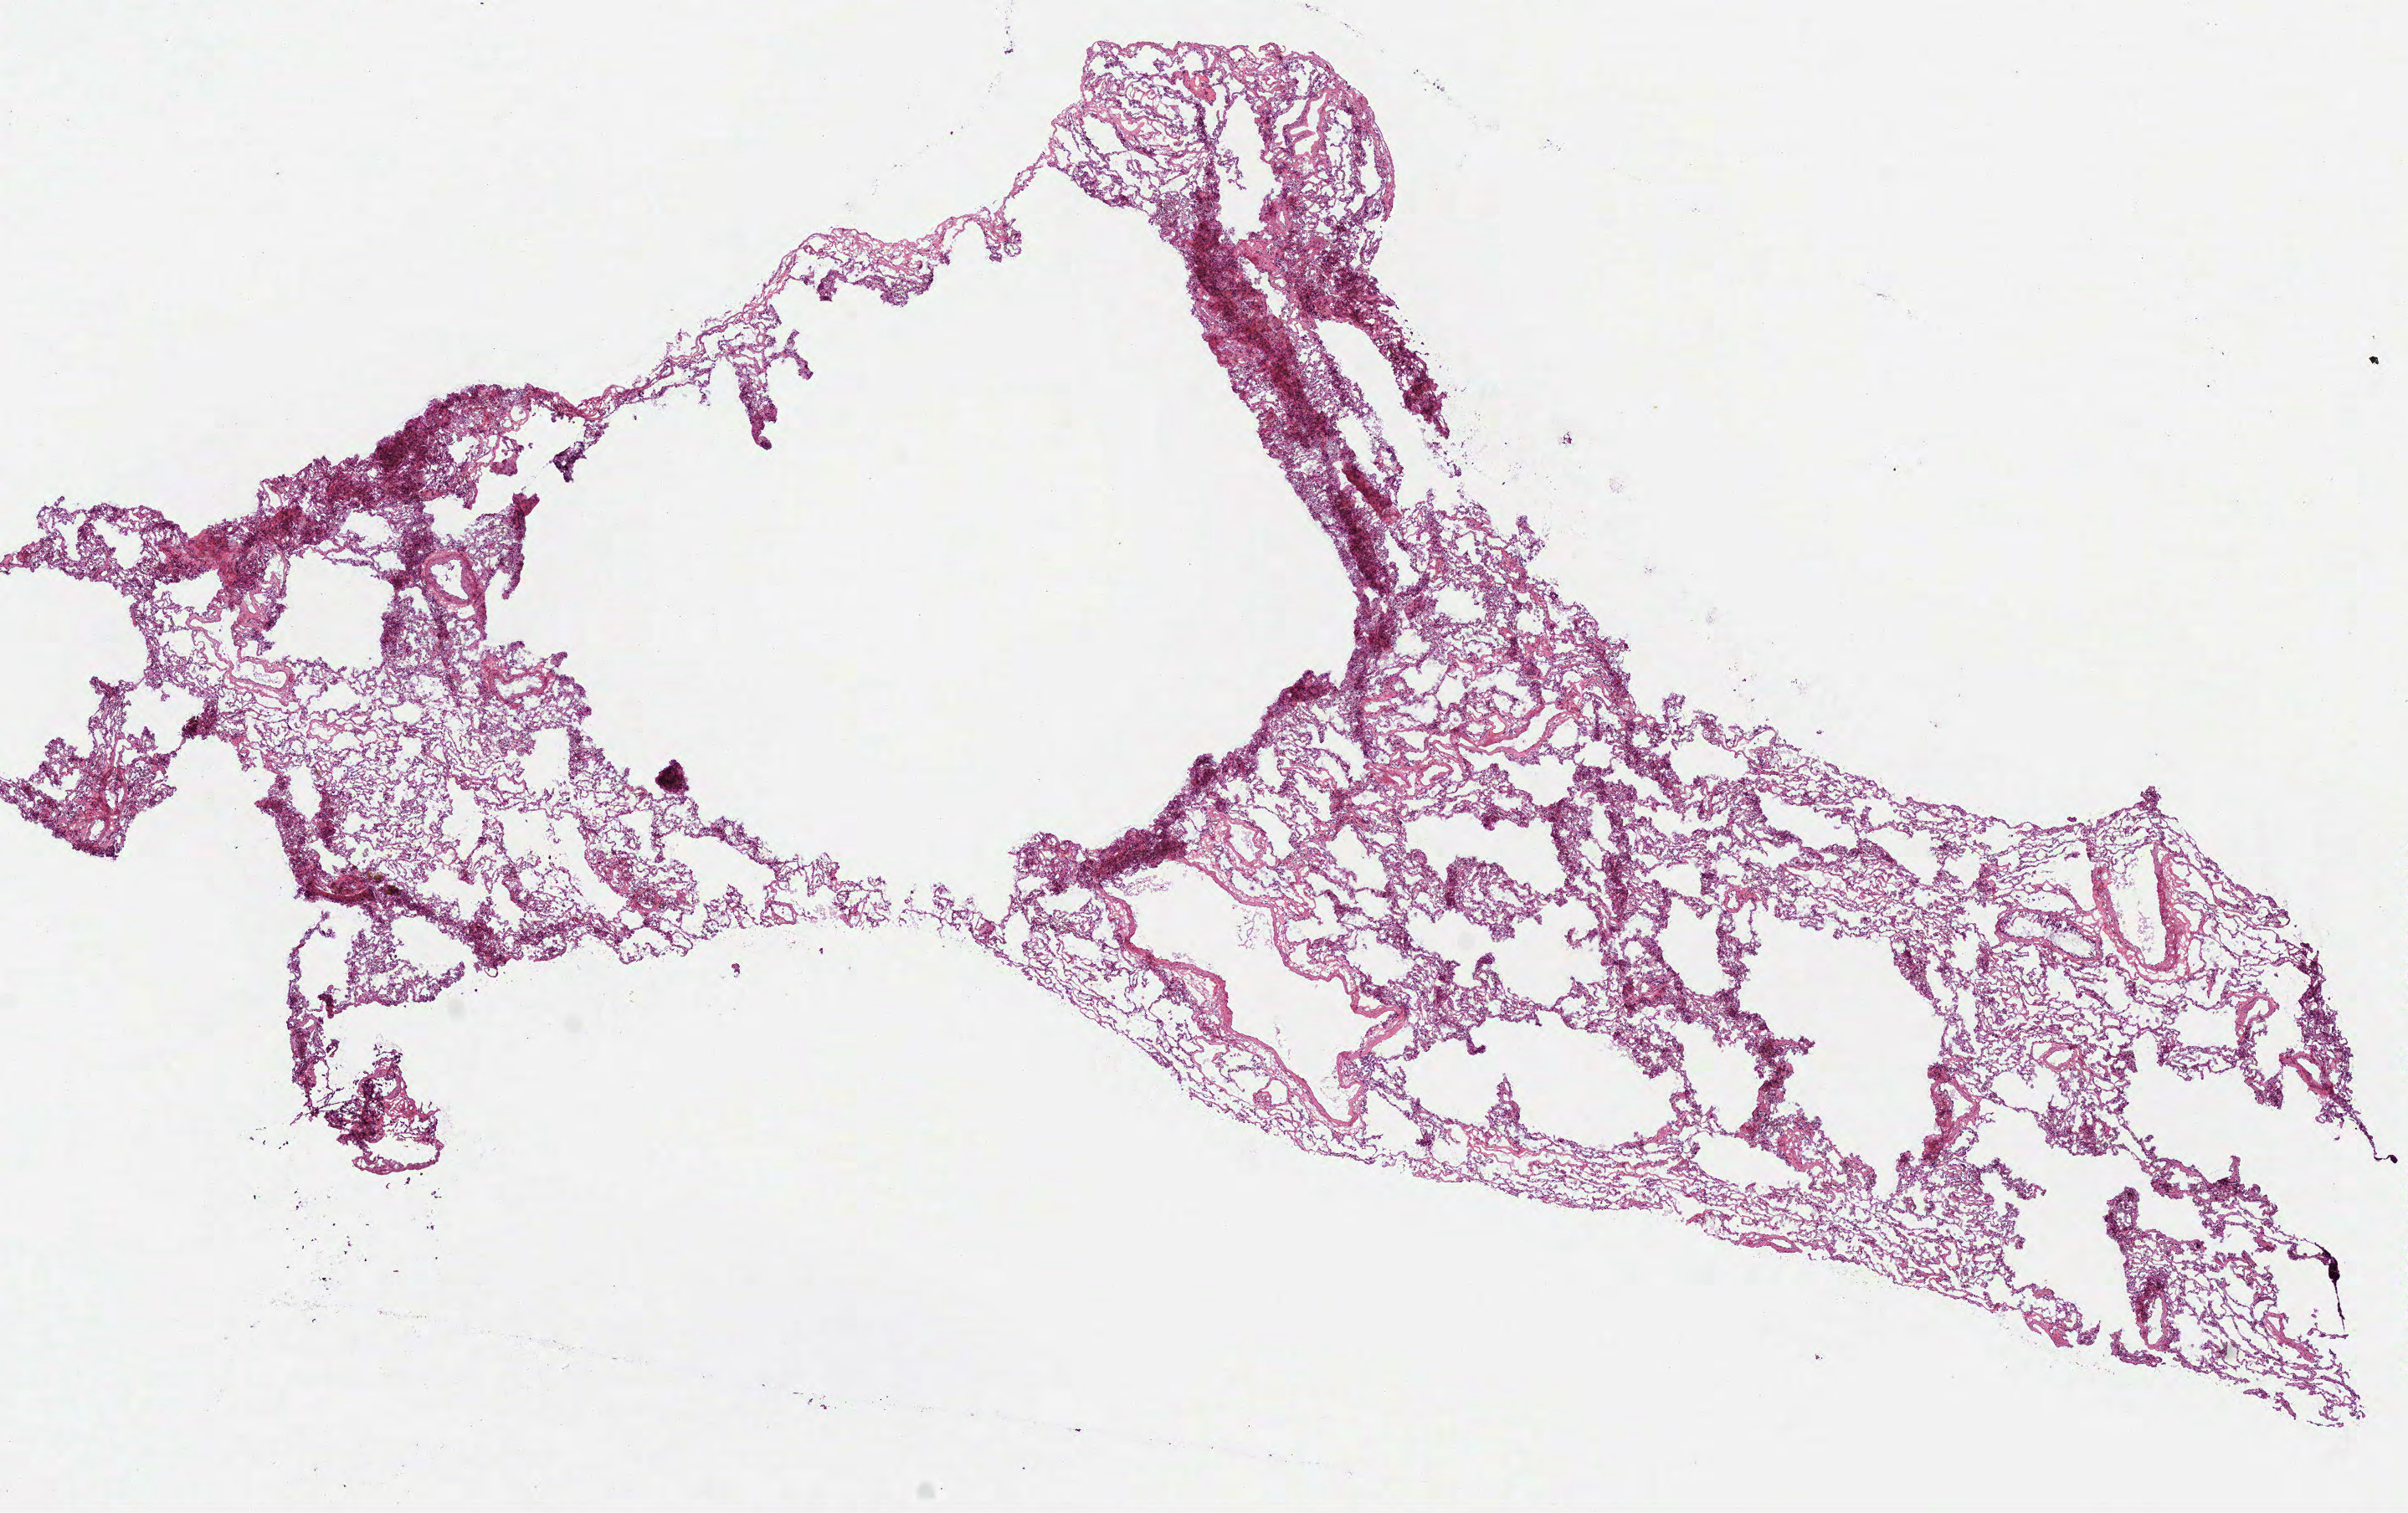
Hematoxylin and eosin (H&E) stained whole-slide image, shown as a low-resolution overview of the whole scanned area (about 11.6 x 7.3 mm); frozen section; solid tissue normal (non-tumour tissue) sample from the lung. Patient: female, age at initial diagnosis 68 years.
• this section: solid tissue normal (non-tumour) sample from the same patient
• patient diagnosis: Adenocarcinoma, NOS (upper lobe, lung)